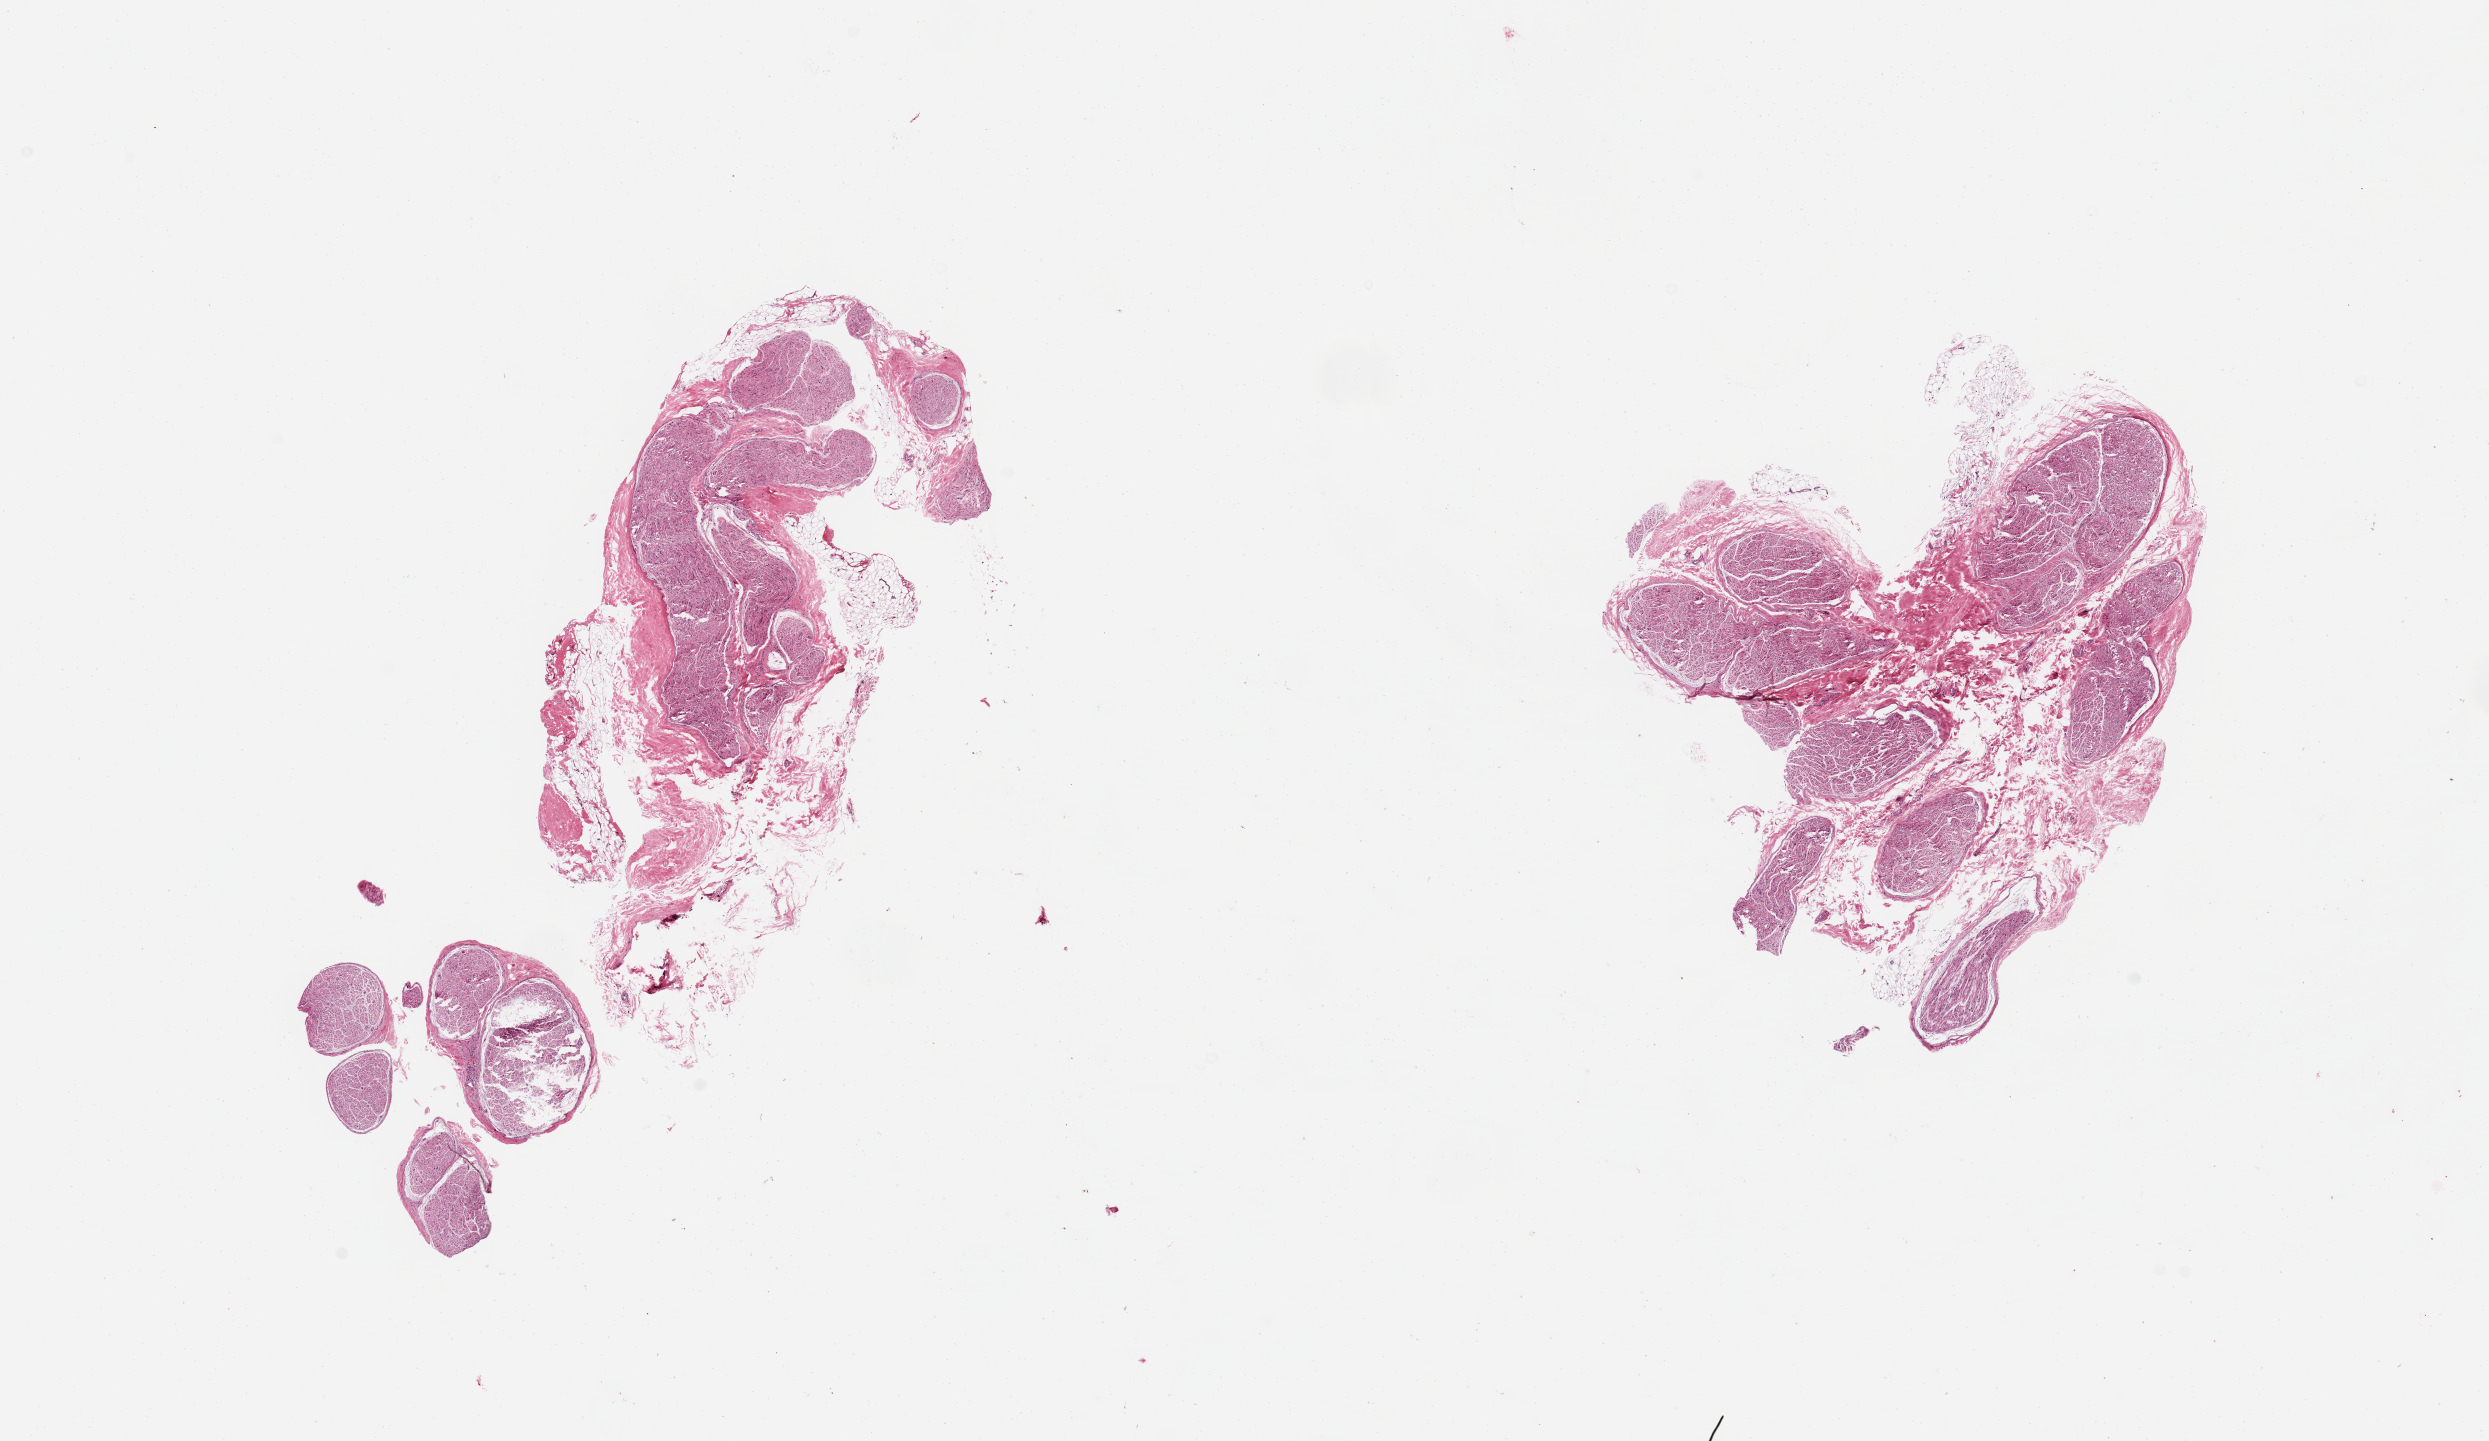
Digitized hematoxylin and eosin (H&E)-stained section, brightfield, shown as a low-resolution overview of the whole scanned area (about 19.7 x 11.4 mm), PAXgene-fixed paraffin-embedded (PFPE) section, sampled site (target tissue): tibial nerve, donor tissue sample. Female donor.
* reviewer comment on this tissue sample: 2 pieces, adherent rims/nubbins of fat up to ~1.5mm